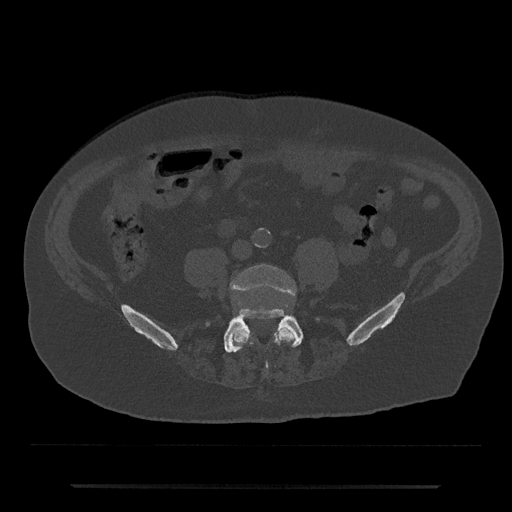
CT including the spine, one axial slice; reconstruction kernel Br40s/3; 120 kVp; bone window (W 1800 / L 400 HU); 512 × 512 image matrix. Patient: male, 80 years. Case-level facts recorded for this patient, not image findings: primary cancer: prostate.
Annotated regions visible in this slice (semi-automatic segmentation, software-assisted and operator-edited):
- L4 vertebra: bounding box [x1, y1, x2, y2] px = [230, 264, 296, 348]
- L5 vertebra: [223, 308, 303, 353]